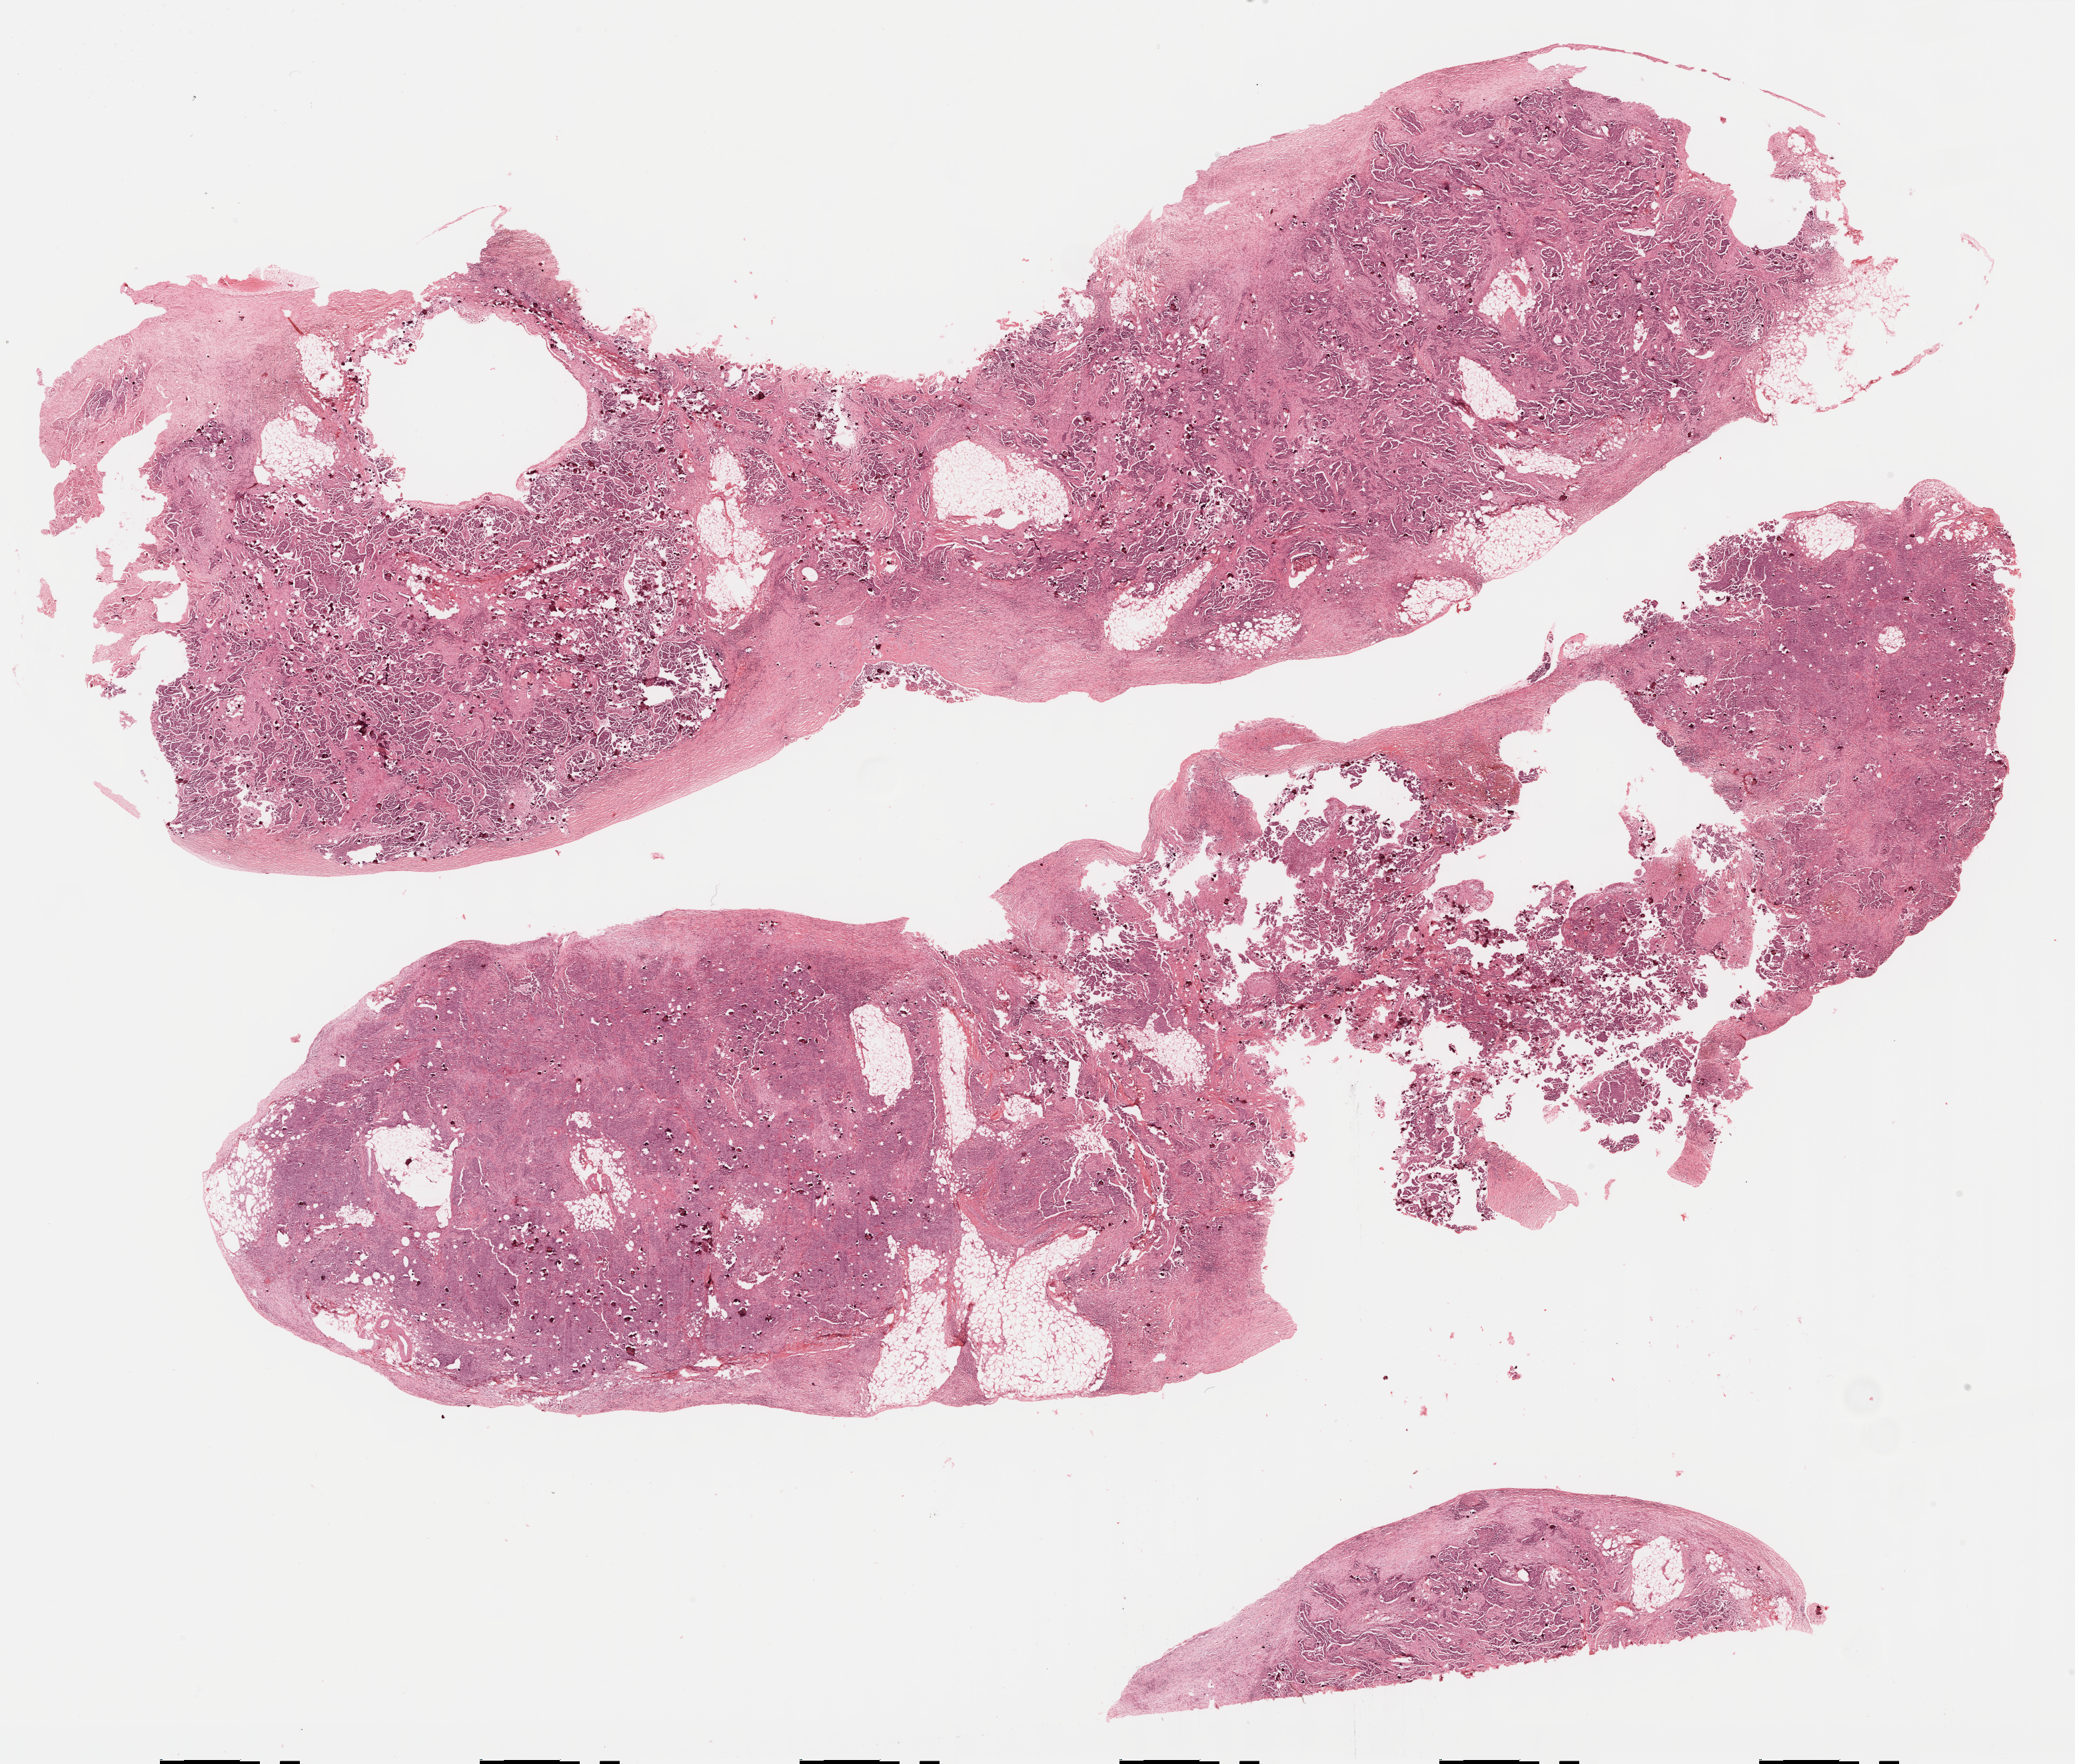
Whole-slide histology image, Hematoxylin and eosin (H&E) stained, shown as a low-resolution overview of the whole scanned area (about 25.1 x 21.4 mm, acquisition: 40x scan), formalin-fixed paraffin-embedded (FFPE) diagnostic section, sample: primary tumour, ovary. Female, age 67 years at initial diagnosis. Histologic grade: G3 (poorly differentiated).
- pathologic diagnosis: Serous cystadenocarcinoma, NOS
- FIGO stage: IIIC